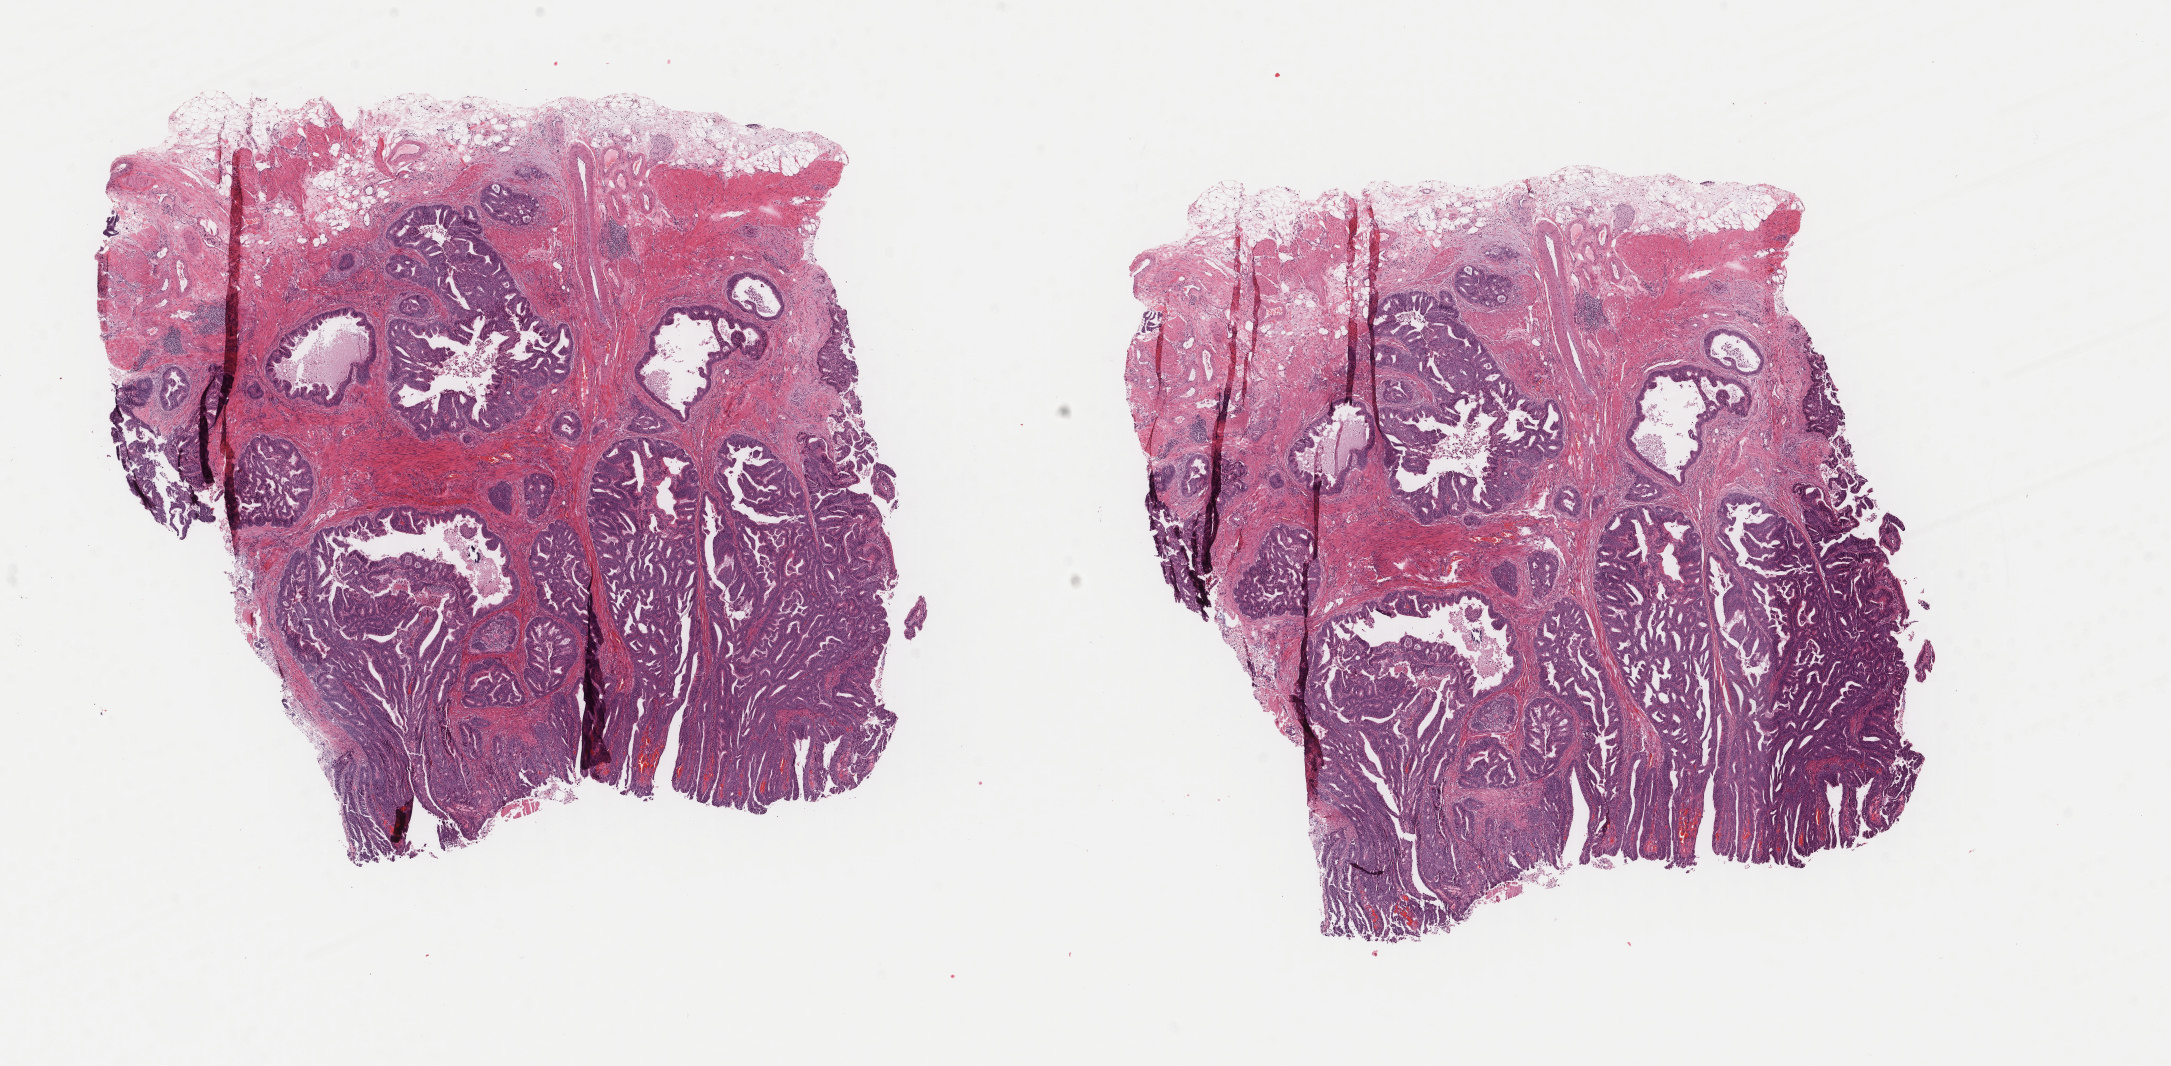
Whole-slide histology image, H&E, shown as a low-resolution overview of the whole scanned area (about 17.2 x 8.5 mm, slide scanned at 40x); frozen section from the bottom of the tissue portion; colon, primary tumour sample. Female, age 68 years at initial diagnosis. Pathologist review of this section (percent, as recorded): tumour cells 60%, tumour nuclei 80%, normal cells 0%, stromal cells 35%, necrosis 5%. Infiltration values recorded for this section: lymphocyte infiltration 0%, monocyte infiltration 0%, neutrophil infiltration 0%.
* diagnosis: Adenocarcinoma, NOS (ascending colon)
* AJCC pathologic stage: IIIC (6th edition)